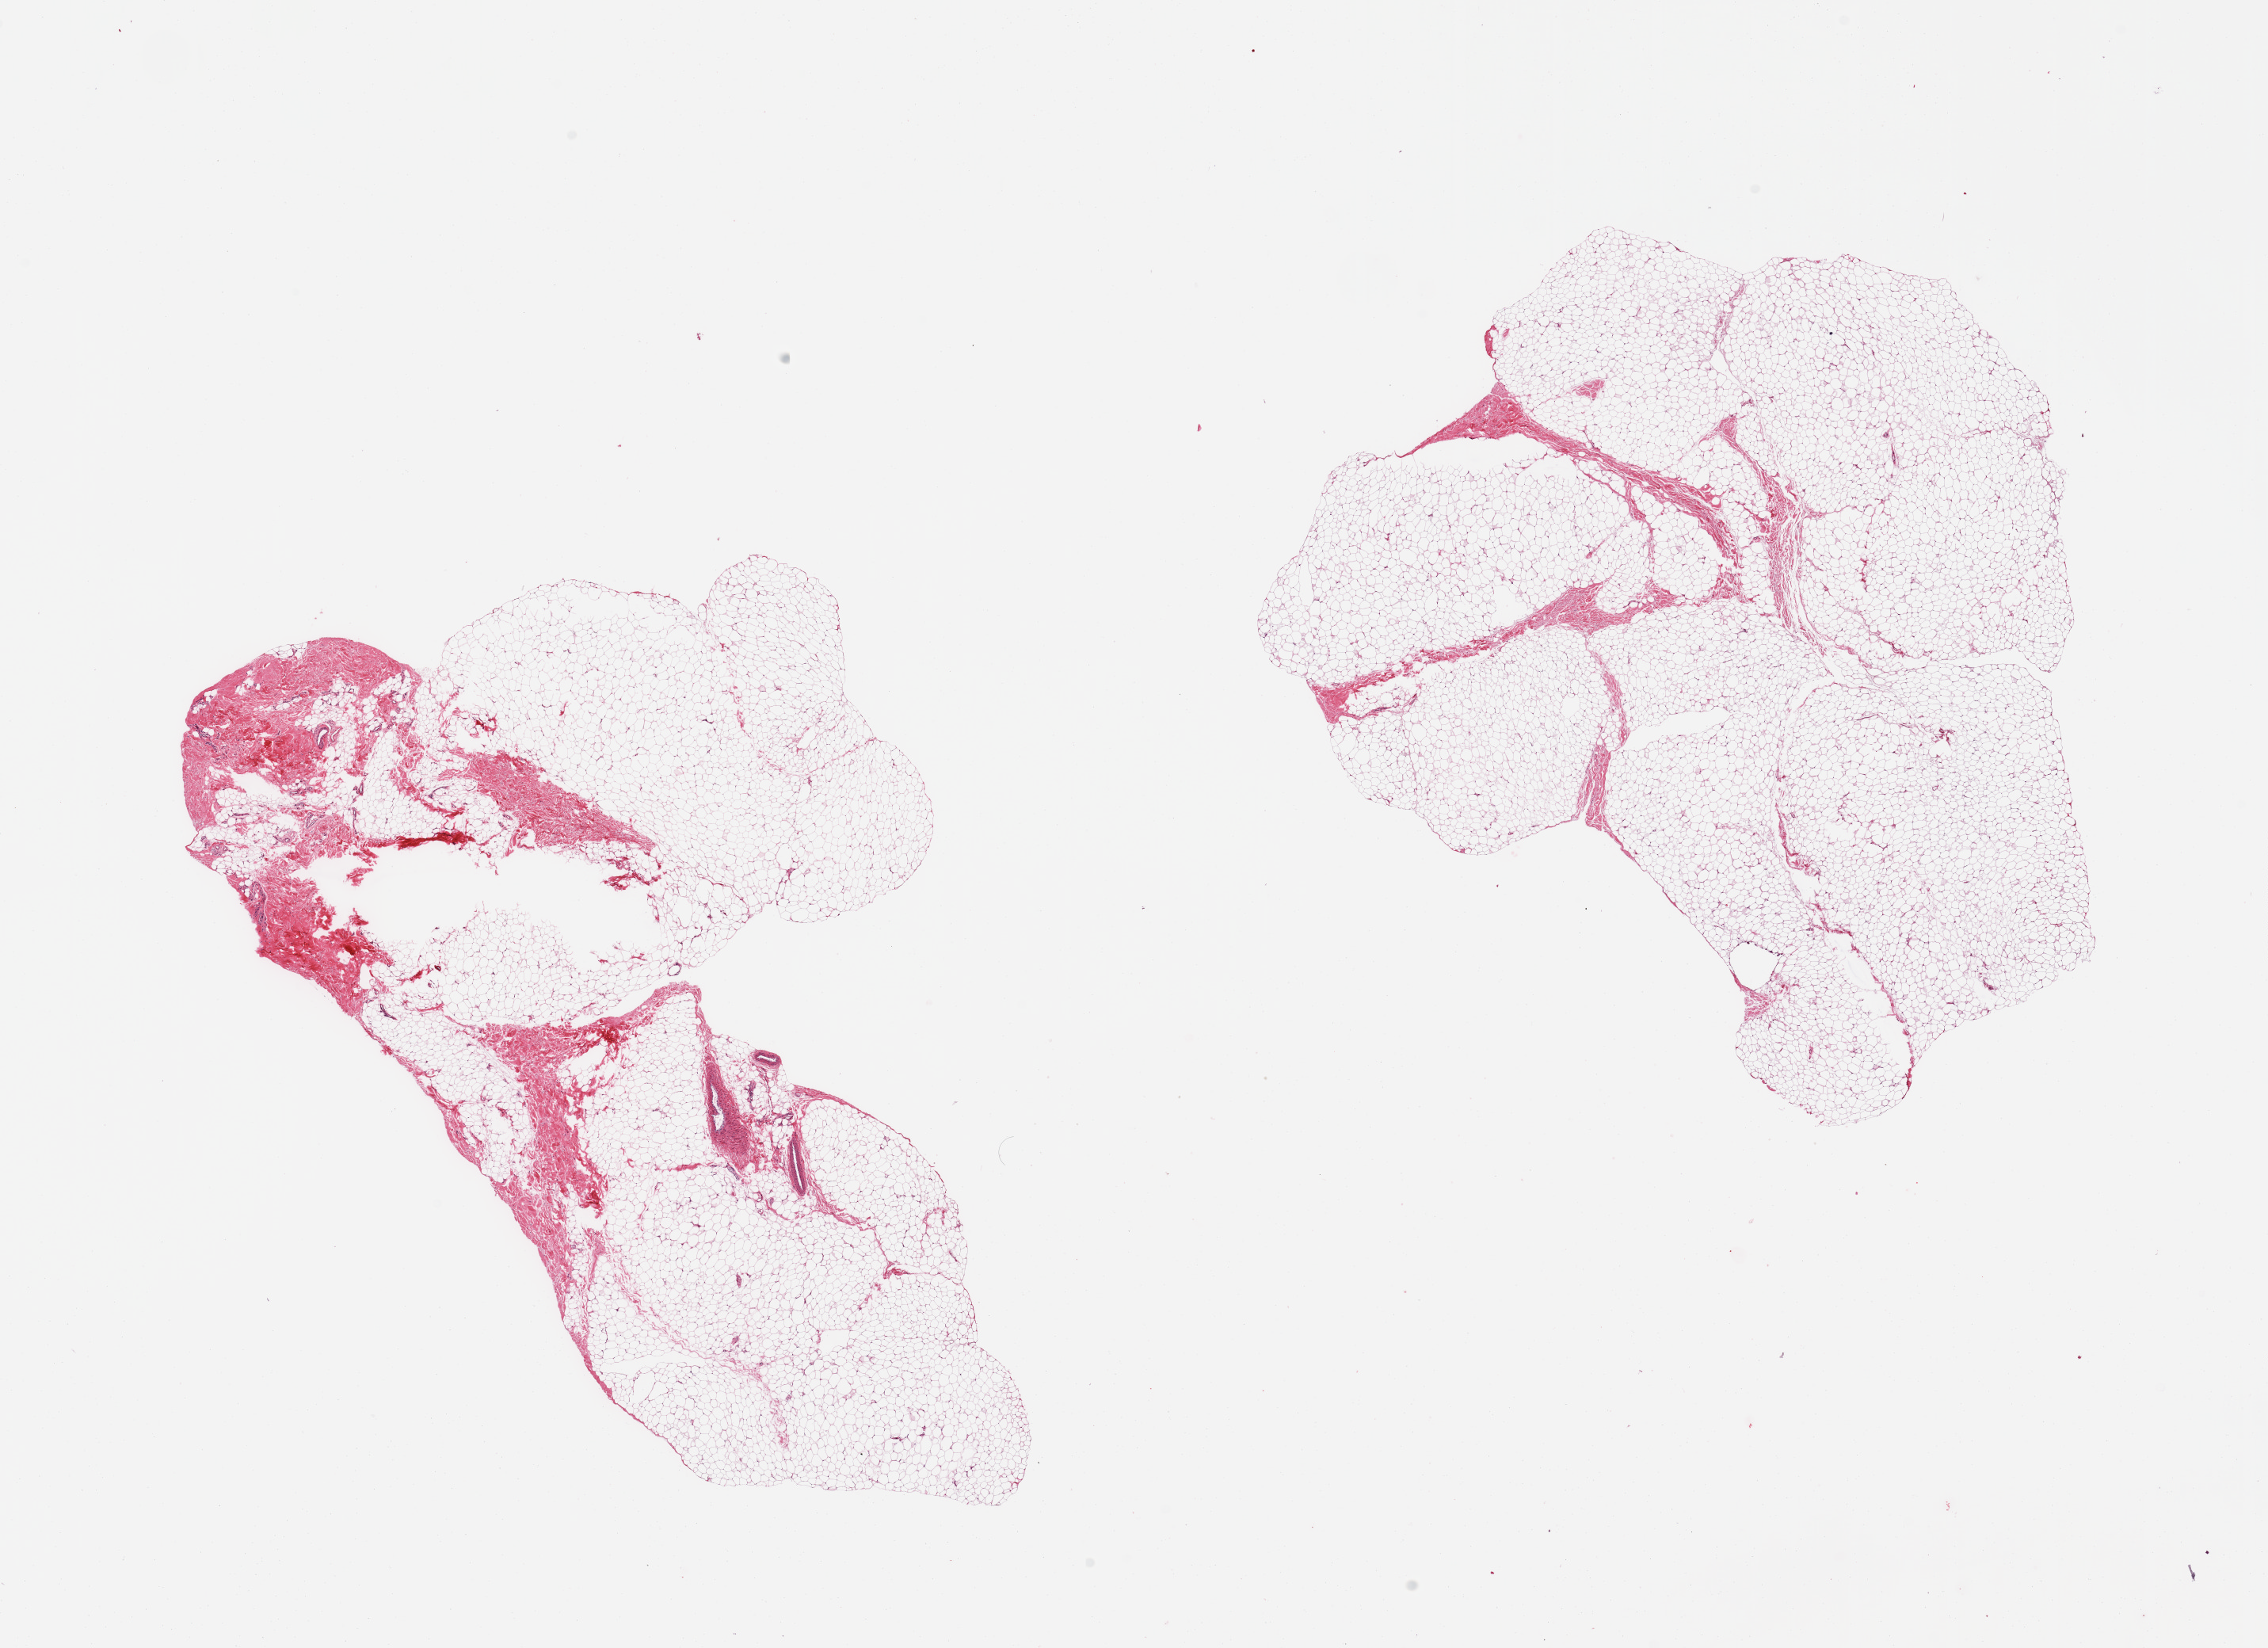
Digitized haematoxylin and eosin-stained section — whole scanned area (about 22.6 x 16.4 mm, from a 20x scan) shown as a low-resolution overview, PAXgene-fixed paraffin-embedded (PFPE) section, section of breast (target tissue), tissue donor sample. Donor sex: male.
Reviewer comment on this tissue sample: 2 pieces; fibroadipose tissue without mammary ducts.